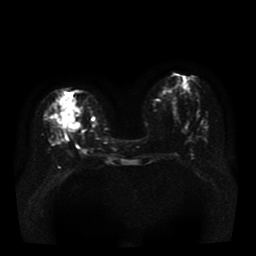
Breast MRI, one axial slice. Diffusion-weighted series; image 2 of 4 stored at this slice position (different b-values; order by instance number). 1.5 T. 5 mm slice thickness. 256 × 256 image matrix, field of view 330 × 330 mm. Female patient.
Outlined on this slice (outlined manually by an expert reader):
- tumour on diffusion-weighted imaging: box from (x=65, y=101) to (x=80, y=131) px